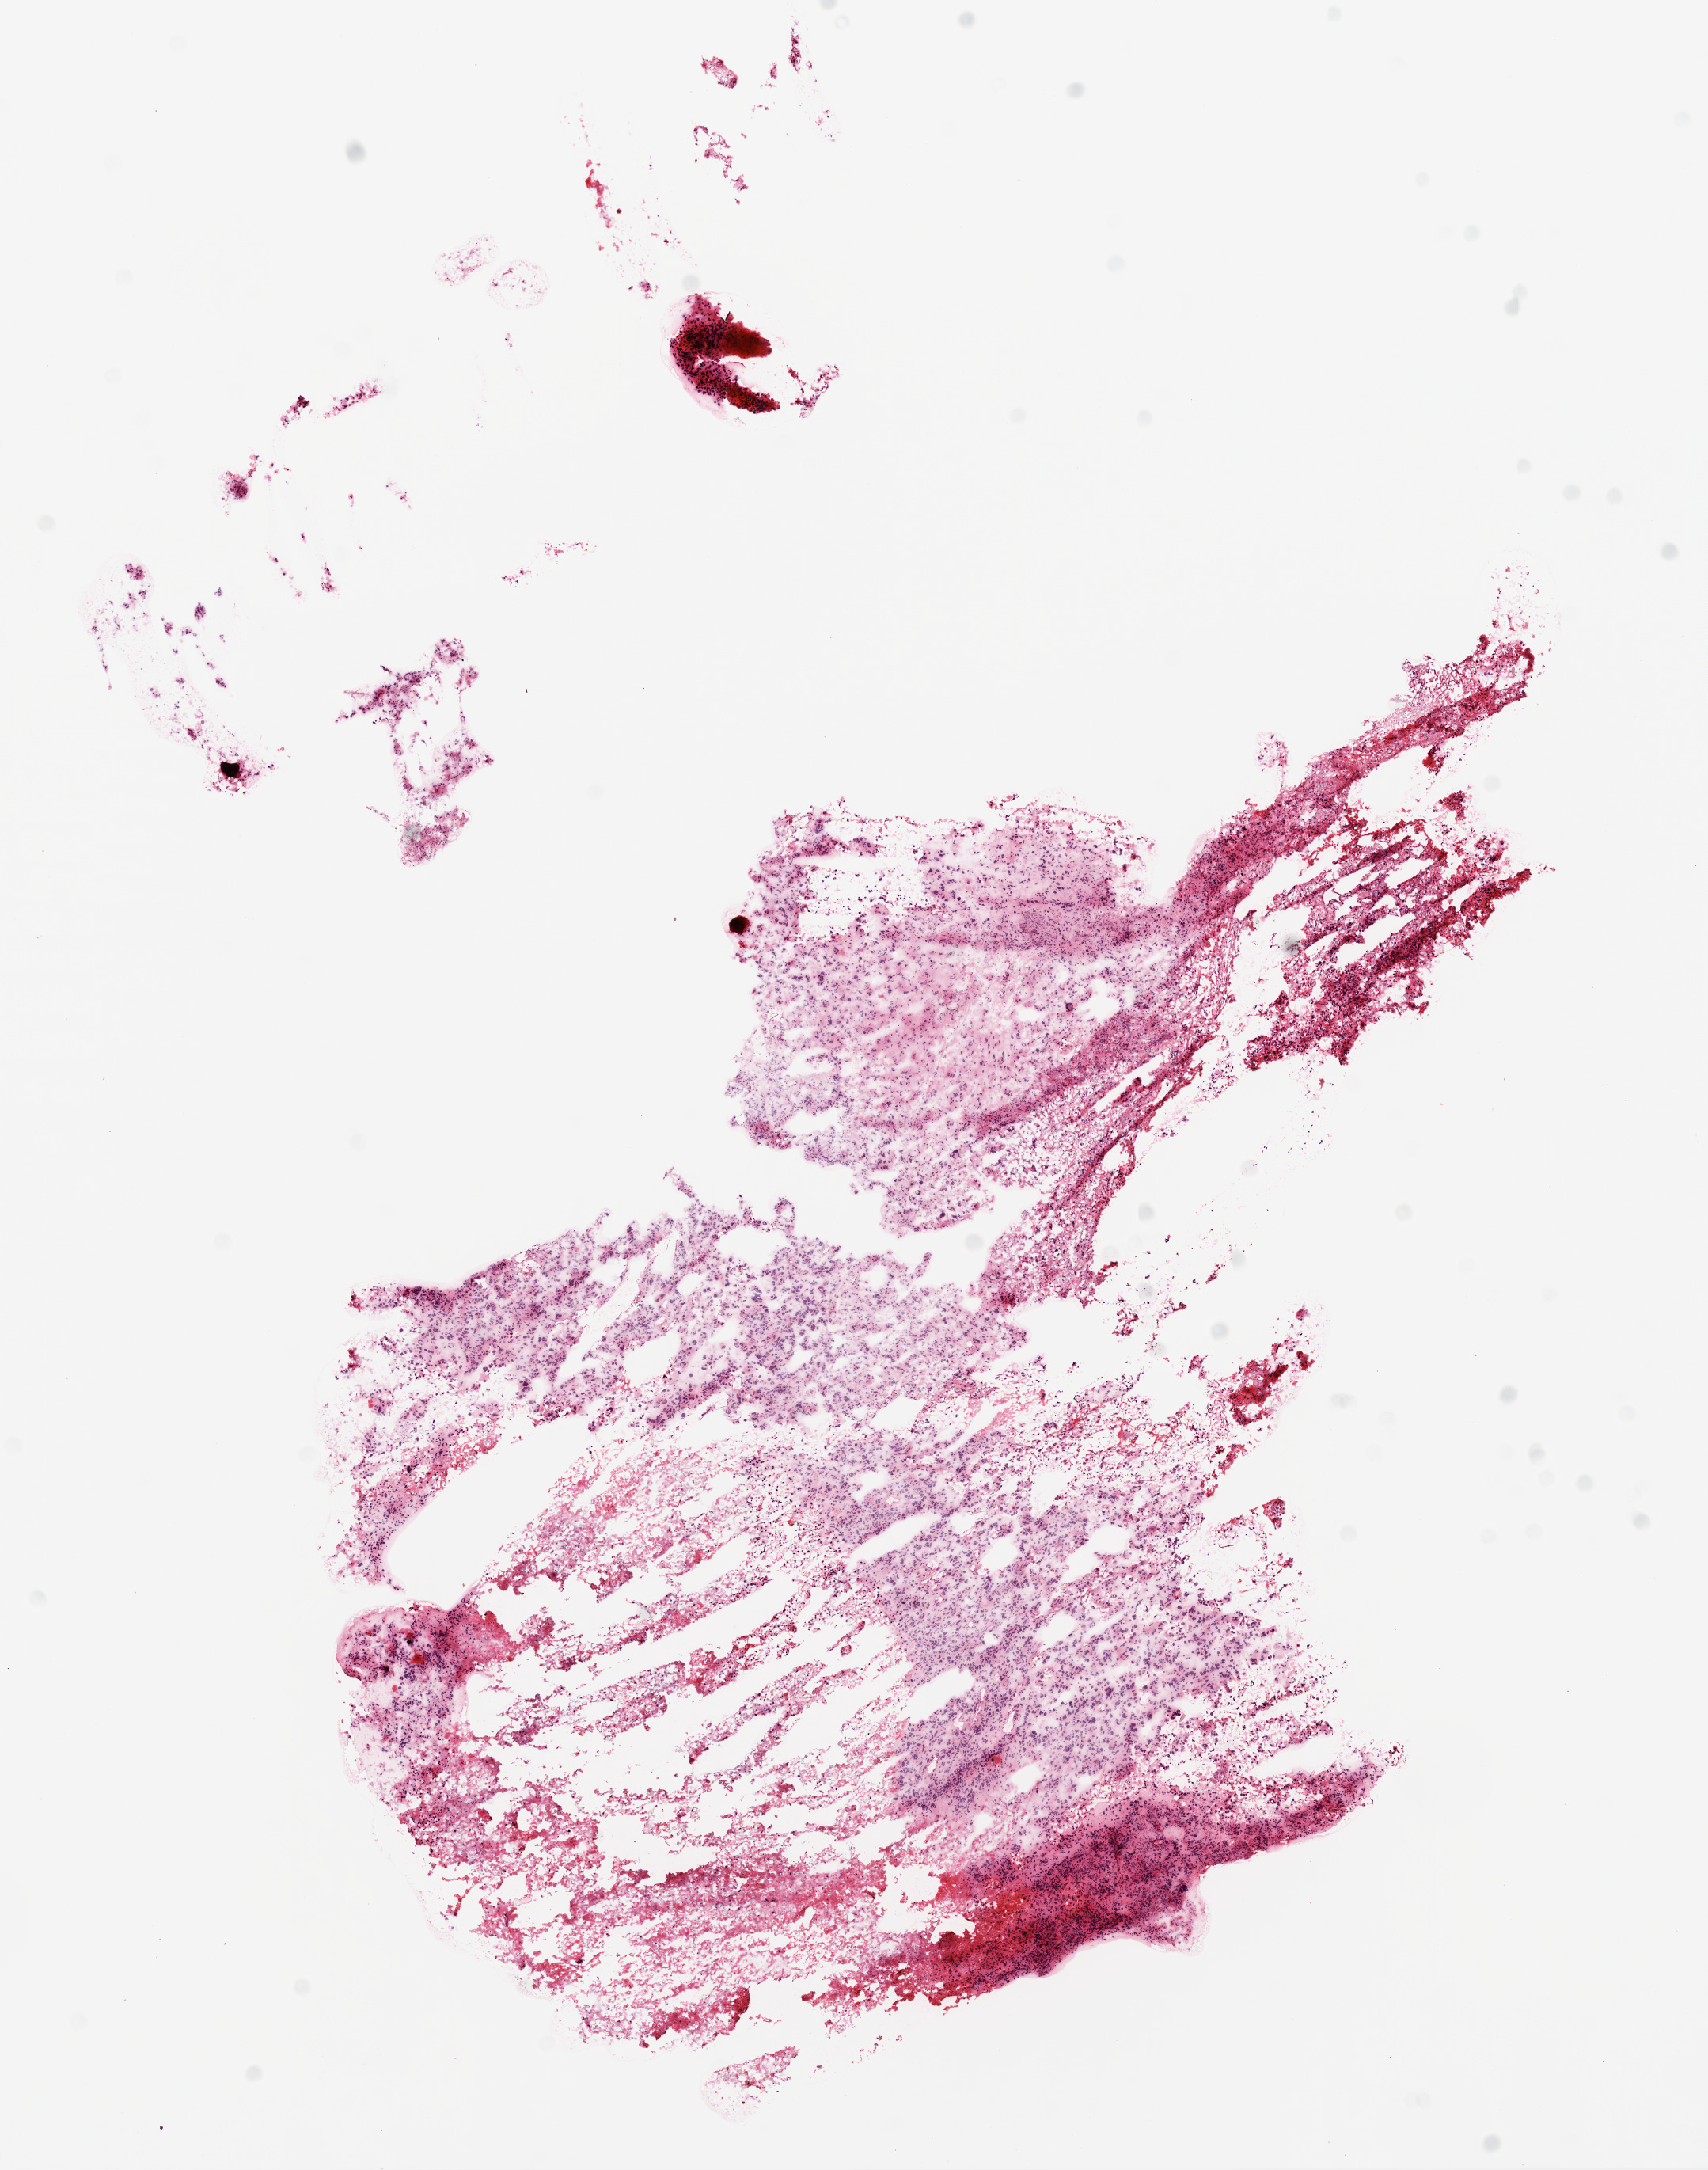
Whole-slide histology image, H&E-stained — whole scanned area (about 8.7 x 11.1 mm) shown as a low-resolution overview, frozen section from the top of the tissue portion, sample: primary tumour, brain. Male patient; age at initial diagnosis 58 years. Pathologist review of this section (percent, as recorded): tumour cells 70%, tumour nuclei 85%, normal cells 0%, stromal cells 0%, necrosis 30%.
Diagnosis: Glioblastoma.